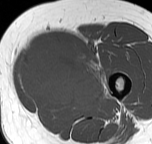
MRI of an extremity soft-tissue mass, one axial slice. Position 22 of 57 along the scan axis. MR volume resampled by the dataset authors to the PET/CT grid (not the native acquisition matrix). 3.27 mm slice thickness. 152 × 144 image matrix, field of view 148 × 141 mm. Female patient. From the clinical record (not read from this slice): histological type: pleiomorphic leiomyosarcoma; grade: intermediate; site of the primary tumour: left thigh.
Annotated regions visible in this slice (expert contour drawn on MRI and transferred to this co-registered scan by the dataset authors):
- gross tumour volume including surrounding oedema: bounding box (x1, y1, x2, y2) in pixels: (16, 42, 108, 113)
- gross tumour volume (mass): (18, 44, 103, 111)